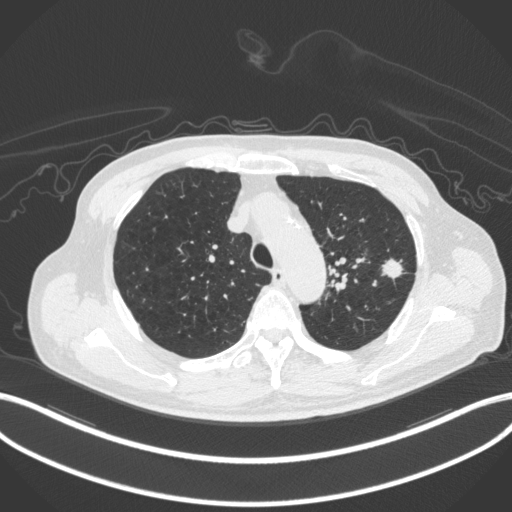
Chest CT, one axial slice; position 338 of 420 along the scan axis; 120 kVp; lung window (W 1500 / L -600 HU); 1 mm slice thickness; 512 × 512 image matrix, field of view 400 × 400 mm. Patient: male, 77 years. From the clinical record (not read from this slice): clinical TNM (as recorded): T3 N1 M0.
Outlined on this slice (rectangle marked by the reading radiologist):
- lung tumour (recorded histology: adenocarcinoma): bounding box [x1, y1, x2, y2] px = [377, 257, 407, 282]